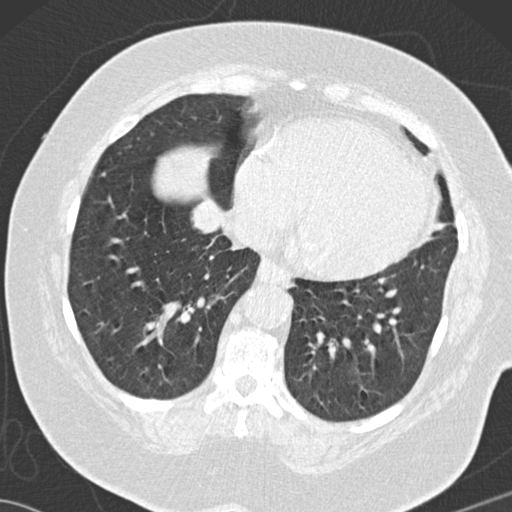
Low-dose screening chest CT, one axial slice. Slice 47 of 146 in the series (ordered by position). 120 kVp. Lung window (W 1500 / L -600 HU). 512 × 512 image matrix, field of view 350 × 350 mm.
Structures marked on this image (manually delineated by an expert):
- lesion 3 (tumor, lower lobe of right lung): bounding box <190,200,225,234> (left, top, right, bottom; pixels)